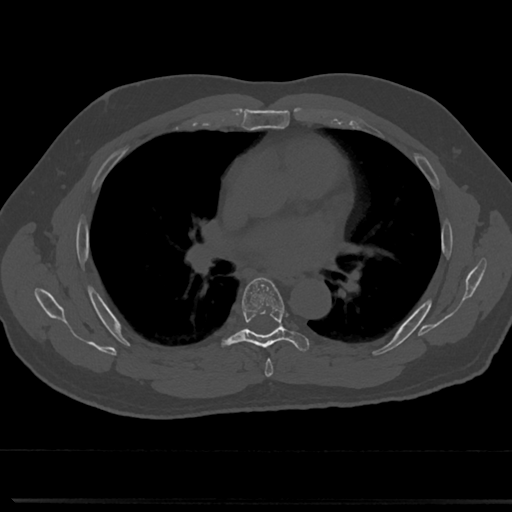
CT including the spine, one axial slice. 120 kVp. Bone window (W 1800 / L 400 HU). 0.5 mm slice thickness. 512 × 512 image matrix, field of view 355 × 355 mm. Patient: male, 61 years. Case-level facts recorded for this patient, not image findings: primary cancer: prostate.
Outlined on this slice (semi-automatically segmented with operator editing):
- T5 vertebra: bounding box (x1, y1, x2, y2) in pixels: (259, 343, 271, 372)
- T6 vertebra: (217, 276, 309, 356)